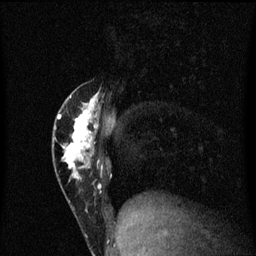
Breast MRI (dynamic contrast-enhanced), one sagittal slice; position 22 of 60 along the scan axis; dynamic contrast-enhanced series, image 2 of 3 at this slice position (ordered by acquisition); 1.5 T; TE 4.2 ms, TR 8.4 ms; 2 mm slice thickness; 256 × 256 image matrix, field of view 200 × 200 mm. Female patient, age 40 years.
Structures marked on this image (semi-automatic segmentation, software-assisted and operator-edited):
- analysis volume of interest (the breast-tissue region the enhancement analysis was run in; not a lesion): bounding box (x1, y1, x2, y2) in pixels: (53, 84, 105, 203)
- tumour enhancement mask (voxels above the 70 % enhancement threshold inside the analysis volume of interest): (53, 92, 104, 179)